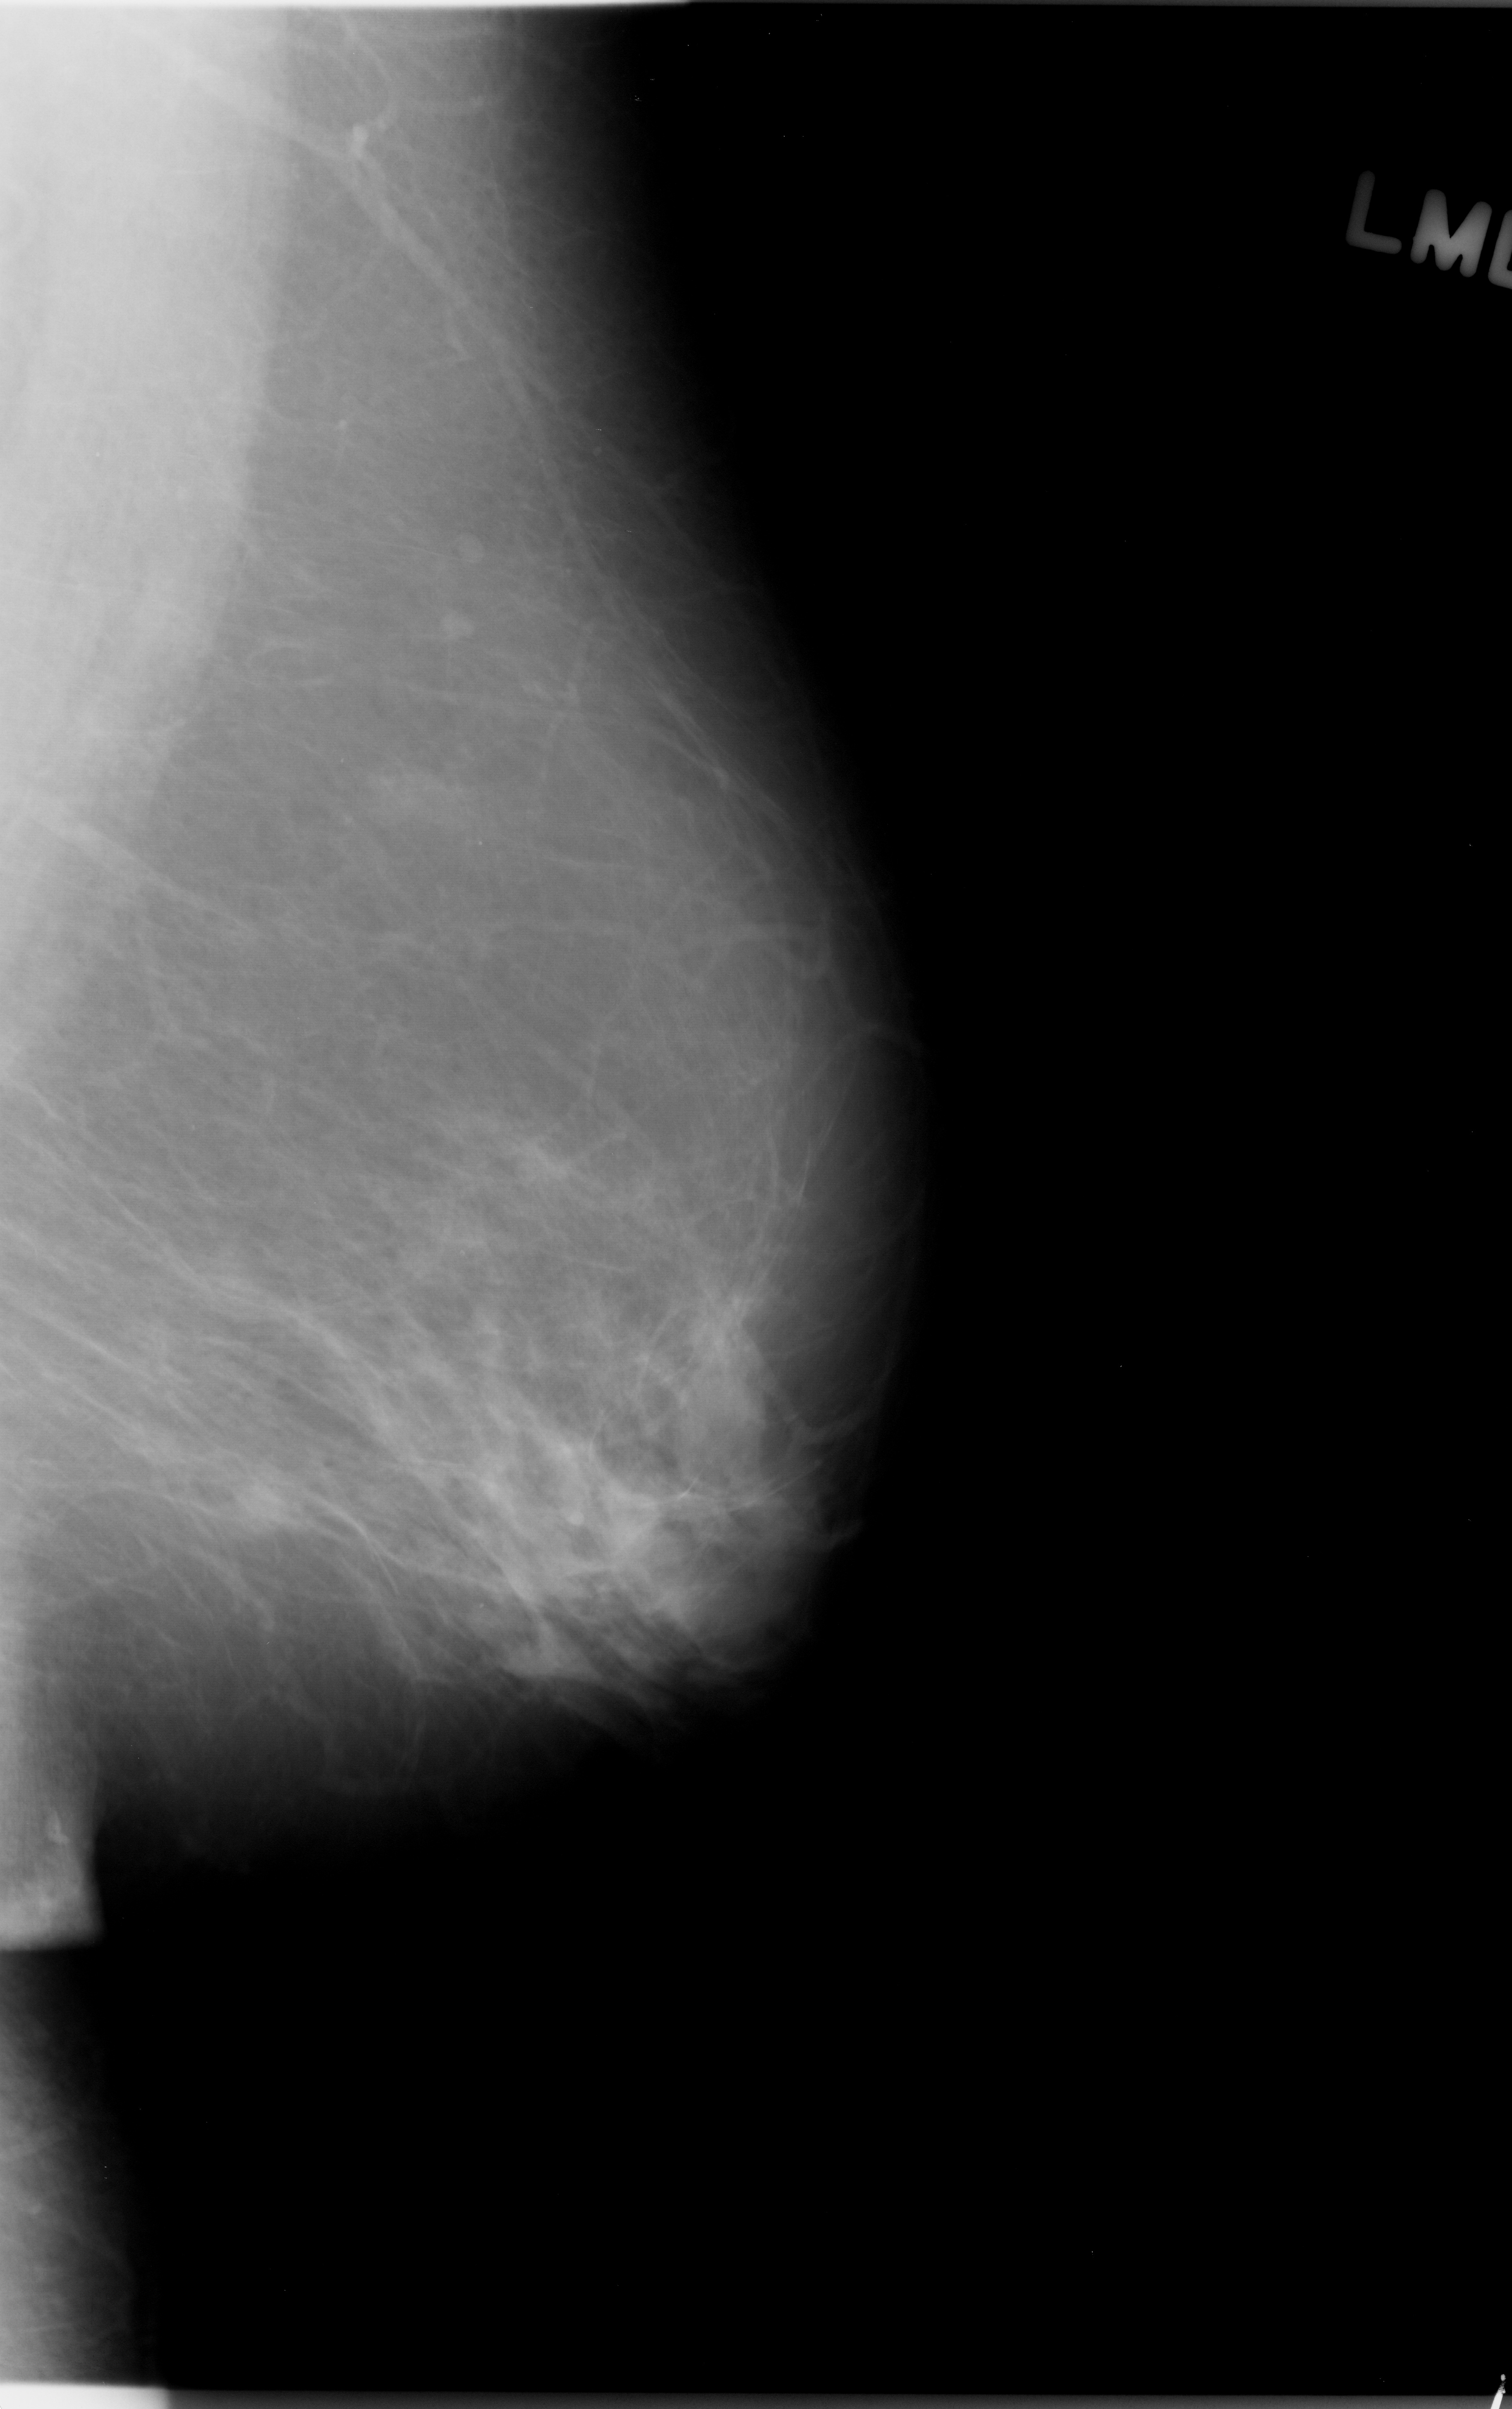
Mammogram (digitized film); left breast; mediolateral oblique (MLO) view; breast composition: almost entirely fatty (BI-RADS density category 1 of 4).
Marked findings (only marked abnormalities are described; nothing is implied about the rest of the image): mass, shape oval, margins ill defined; BI-RADS assessment category 5; subtlety rating 2 on a 1 (subtle) to 5 (obvious) scale; pathology result (as recorded, not read from the image): malignant.